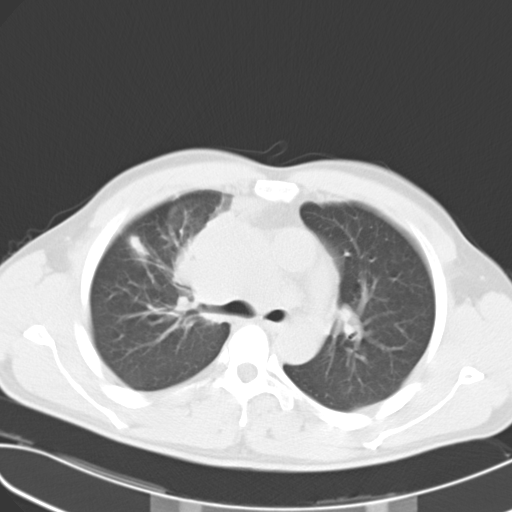
Chest CT, one axial slice; slice 18 of 27 in the series (ordered by position); reconstruction kernel B40f; 120 kVp; lung window (W 1500 / L -600 HU); 10 mm slice thickness; 512 × 512 image matrix, field of view 346 × 346 mm. Male patient, age 32 years. From the clinical record (not read from this slice): clinical TNM (as recorded): T4 N3 M0; histopathological grade: G3.
Annotated regions visible in this slice (rectangle marked by the reading radiologist):
- lung tumour (recorded histology: small cell carcinoma): bounding box <169,207,228,333> (left, top, right, bottom; pixels)